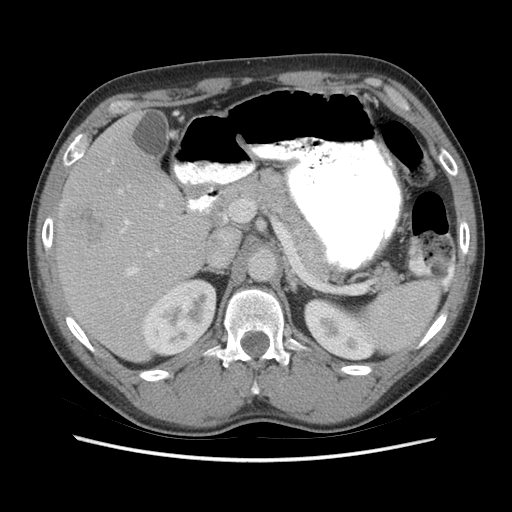
Contrast-enhanced abdominal CT (liver protocol), one axial slice. Reconstruction kernel STANDARD. 140 kVp. Soft-tissue window (W 400 / L 40 HU). 2.5 mm slice thickness. 512 × 512 image matrix, field of view 360 × 360 mm. Case-level facts recorded for this patient, not image findings: diagnosis: hepatocellular carcinoma (patient treated with transarterial chemoembolisation; whether this scan precedes or follows treatment is not stated here); TNM stage (as recorded): Stage-IIIA.
Outlined on this slice (semi-automatically segmented with operator editing):
- liver parenchyma outside the tumour (the mass and vessels are separate outlines, so this box may not span the whole liver): bounding box [x1, y1, x2, y2] px = [54, 112, 238, 362]
- mass: [63, 207, 106, 249]
- liver vessels: [119, 190, 228, 276]